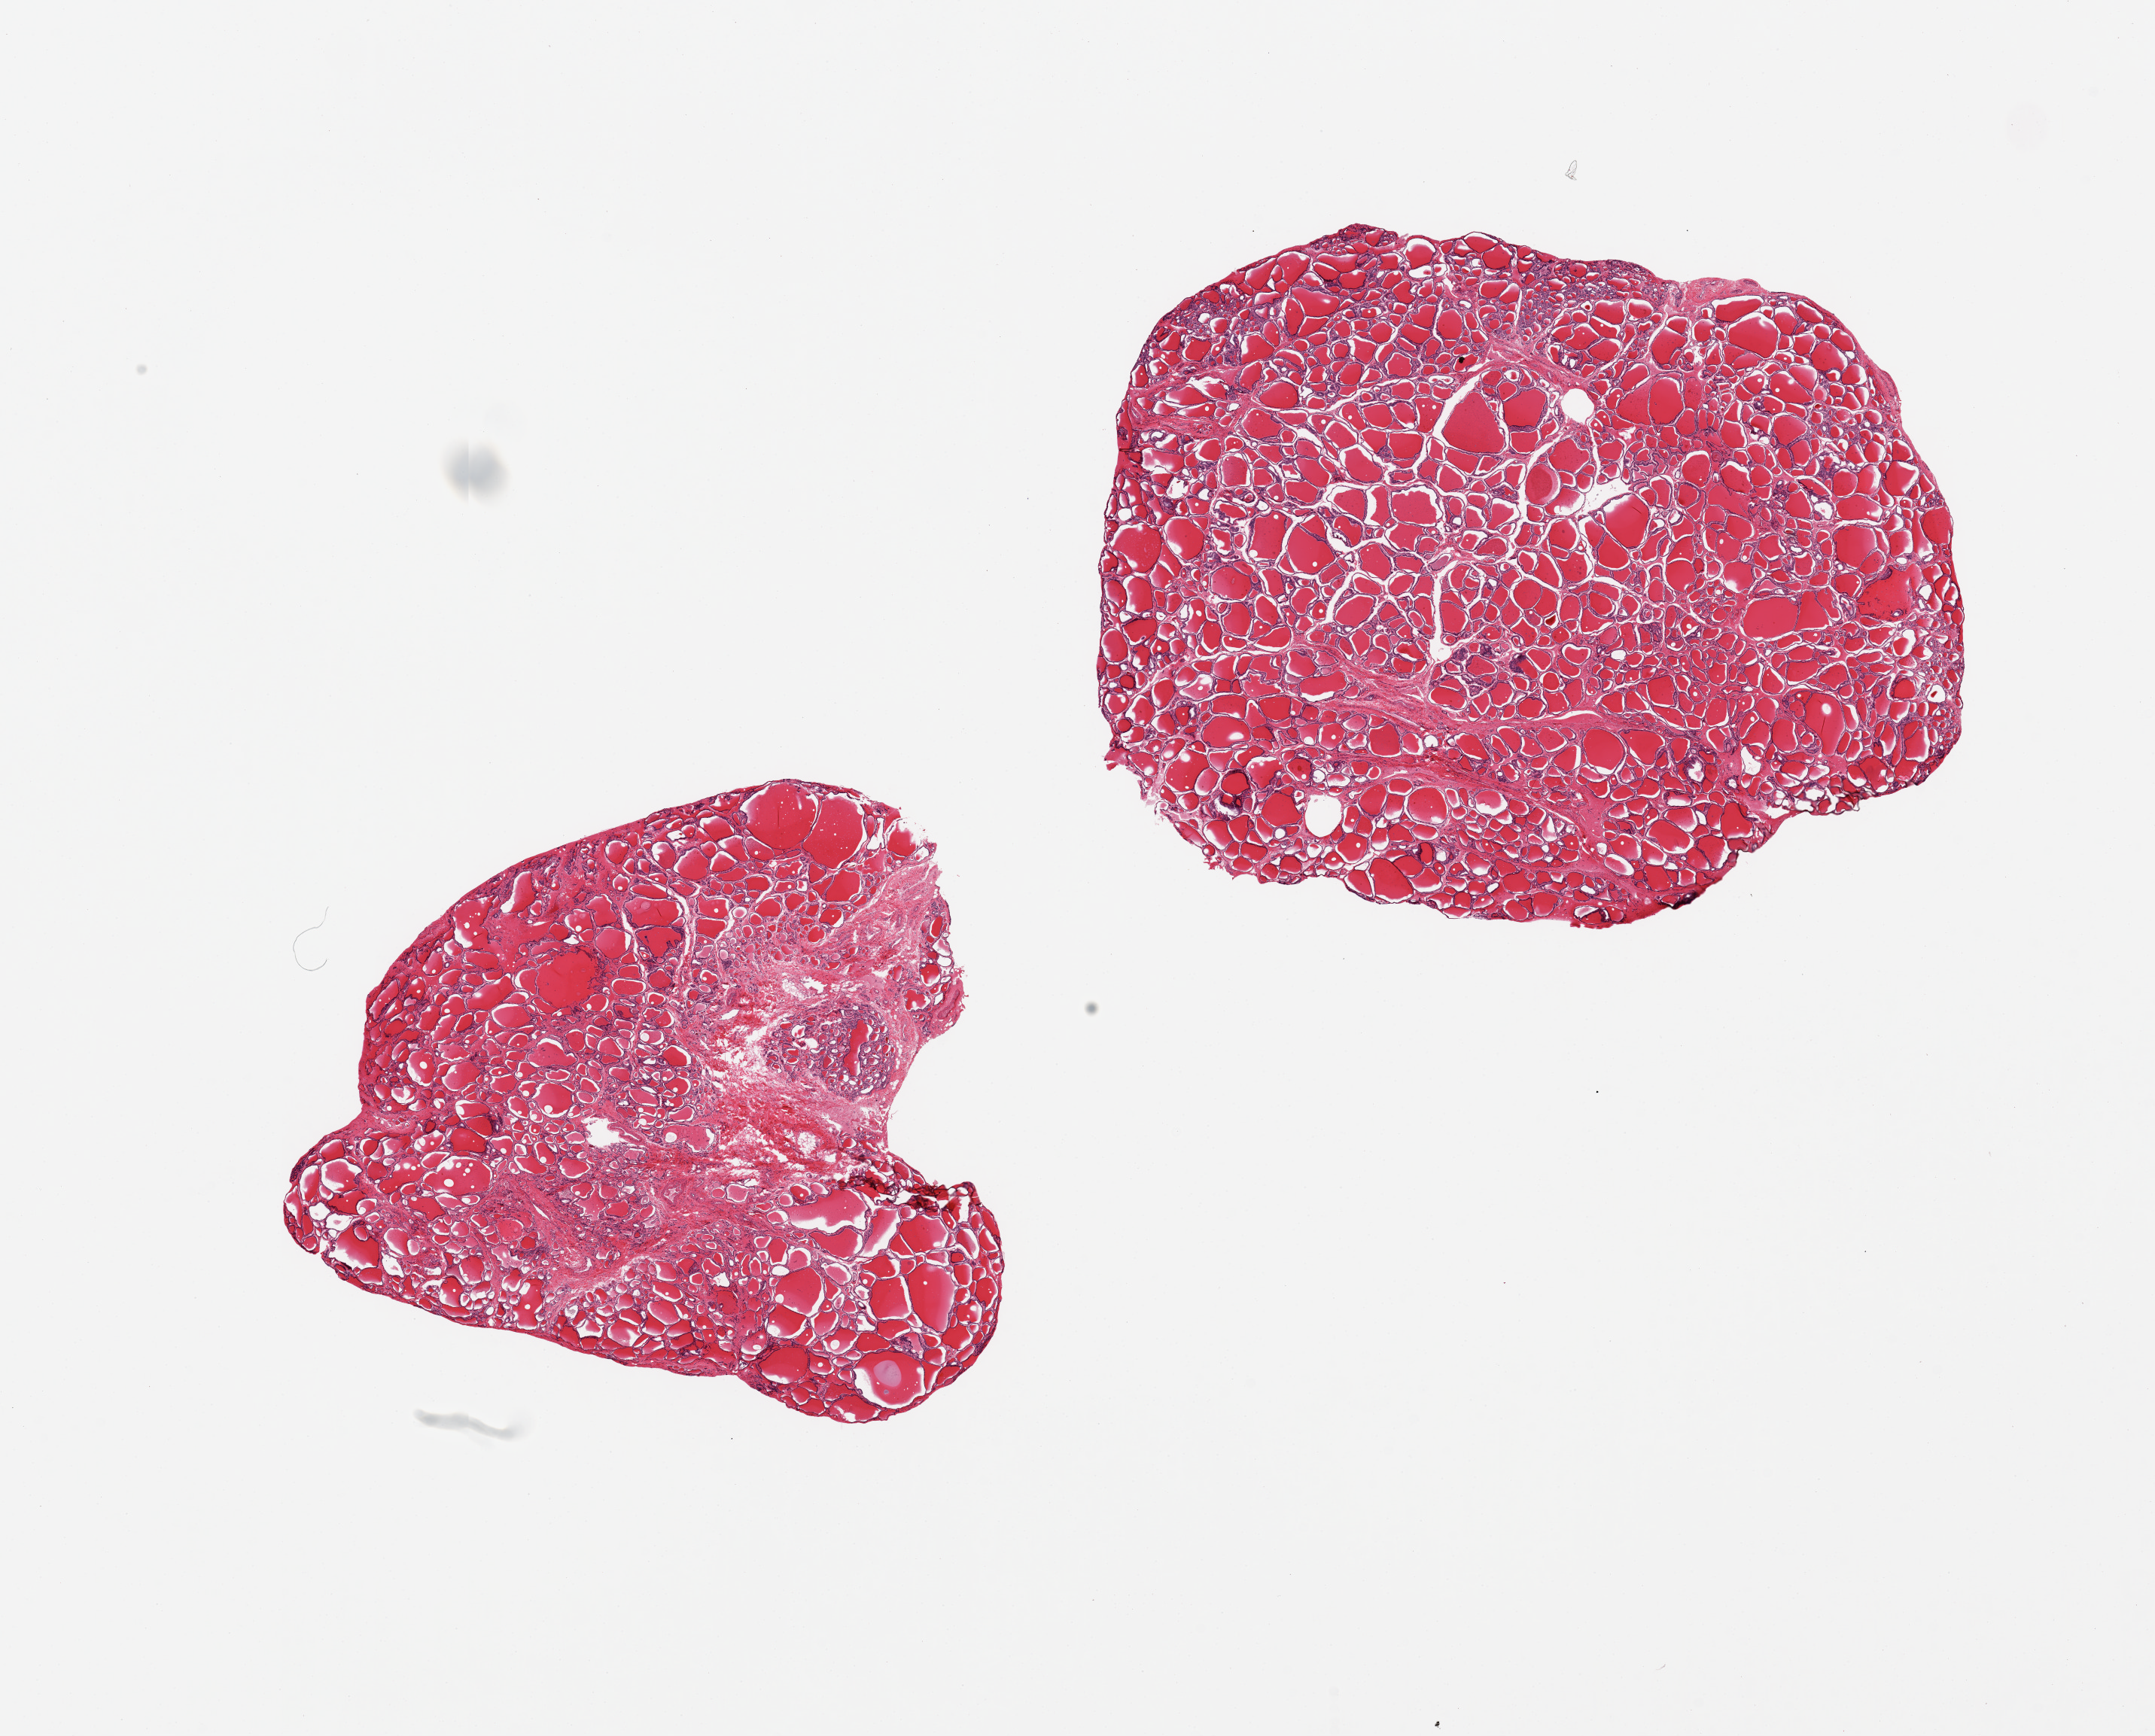
Whole-slide image, H&E stain, brightfield, whole scanned area (about 22.6 x 18.2 mm, slide scanned at 20x) shown as a low-resolution overview, PAXgene-fixed paraffin-embedded (PFPE) section, sampled site (target tissue): thyroid, donor tissue sample. Donor sex: female.
- reviewer comment on this tissue sample: 2 pieces, regressive changes, focal goitrous features